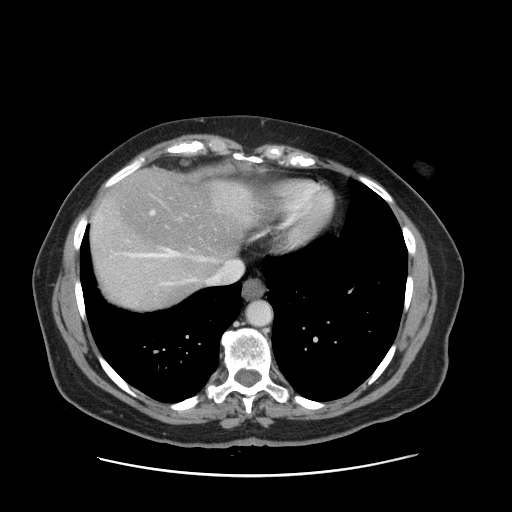
Contrast-enhanced abdominal CT, one axial slice. Position 135 of 161 along the scan axis. Intravenous contrast given. Soft-tissue window (W 400 / L 40 HU). 2.5 mm slice thickness. 512 × 512 image matrix, field of view 398 × 398 mm. Female patient, age 62 years. From the clinical record (not read from this slice): diagnosis: colorectal cancer liver metastases, imaged before liver resection; multiple liver metastases: no; largest metastasis: 2.5 cm.
Annotated regions visible in this slice (expert manual segmentation):
- hepatic veins: box from (x=124, y=191) to (x=242, y=285) px
- liver: (x=92, y=170)–(x=259, y=309)
- planned liver remnant (the part of the liver to remain after resection): (x=96, y=170)–(x=260, y=276)
- portal vein (with intrahepatic branches): (x=151, y=211)–(x=156, y=215)